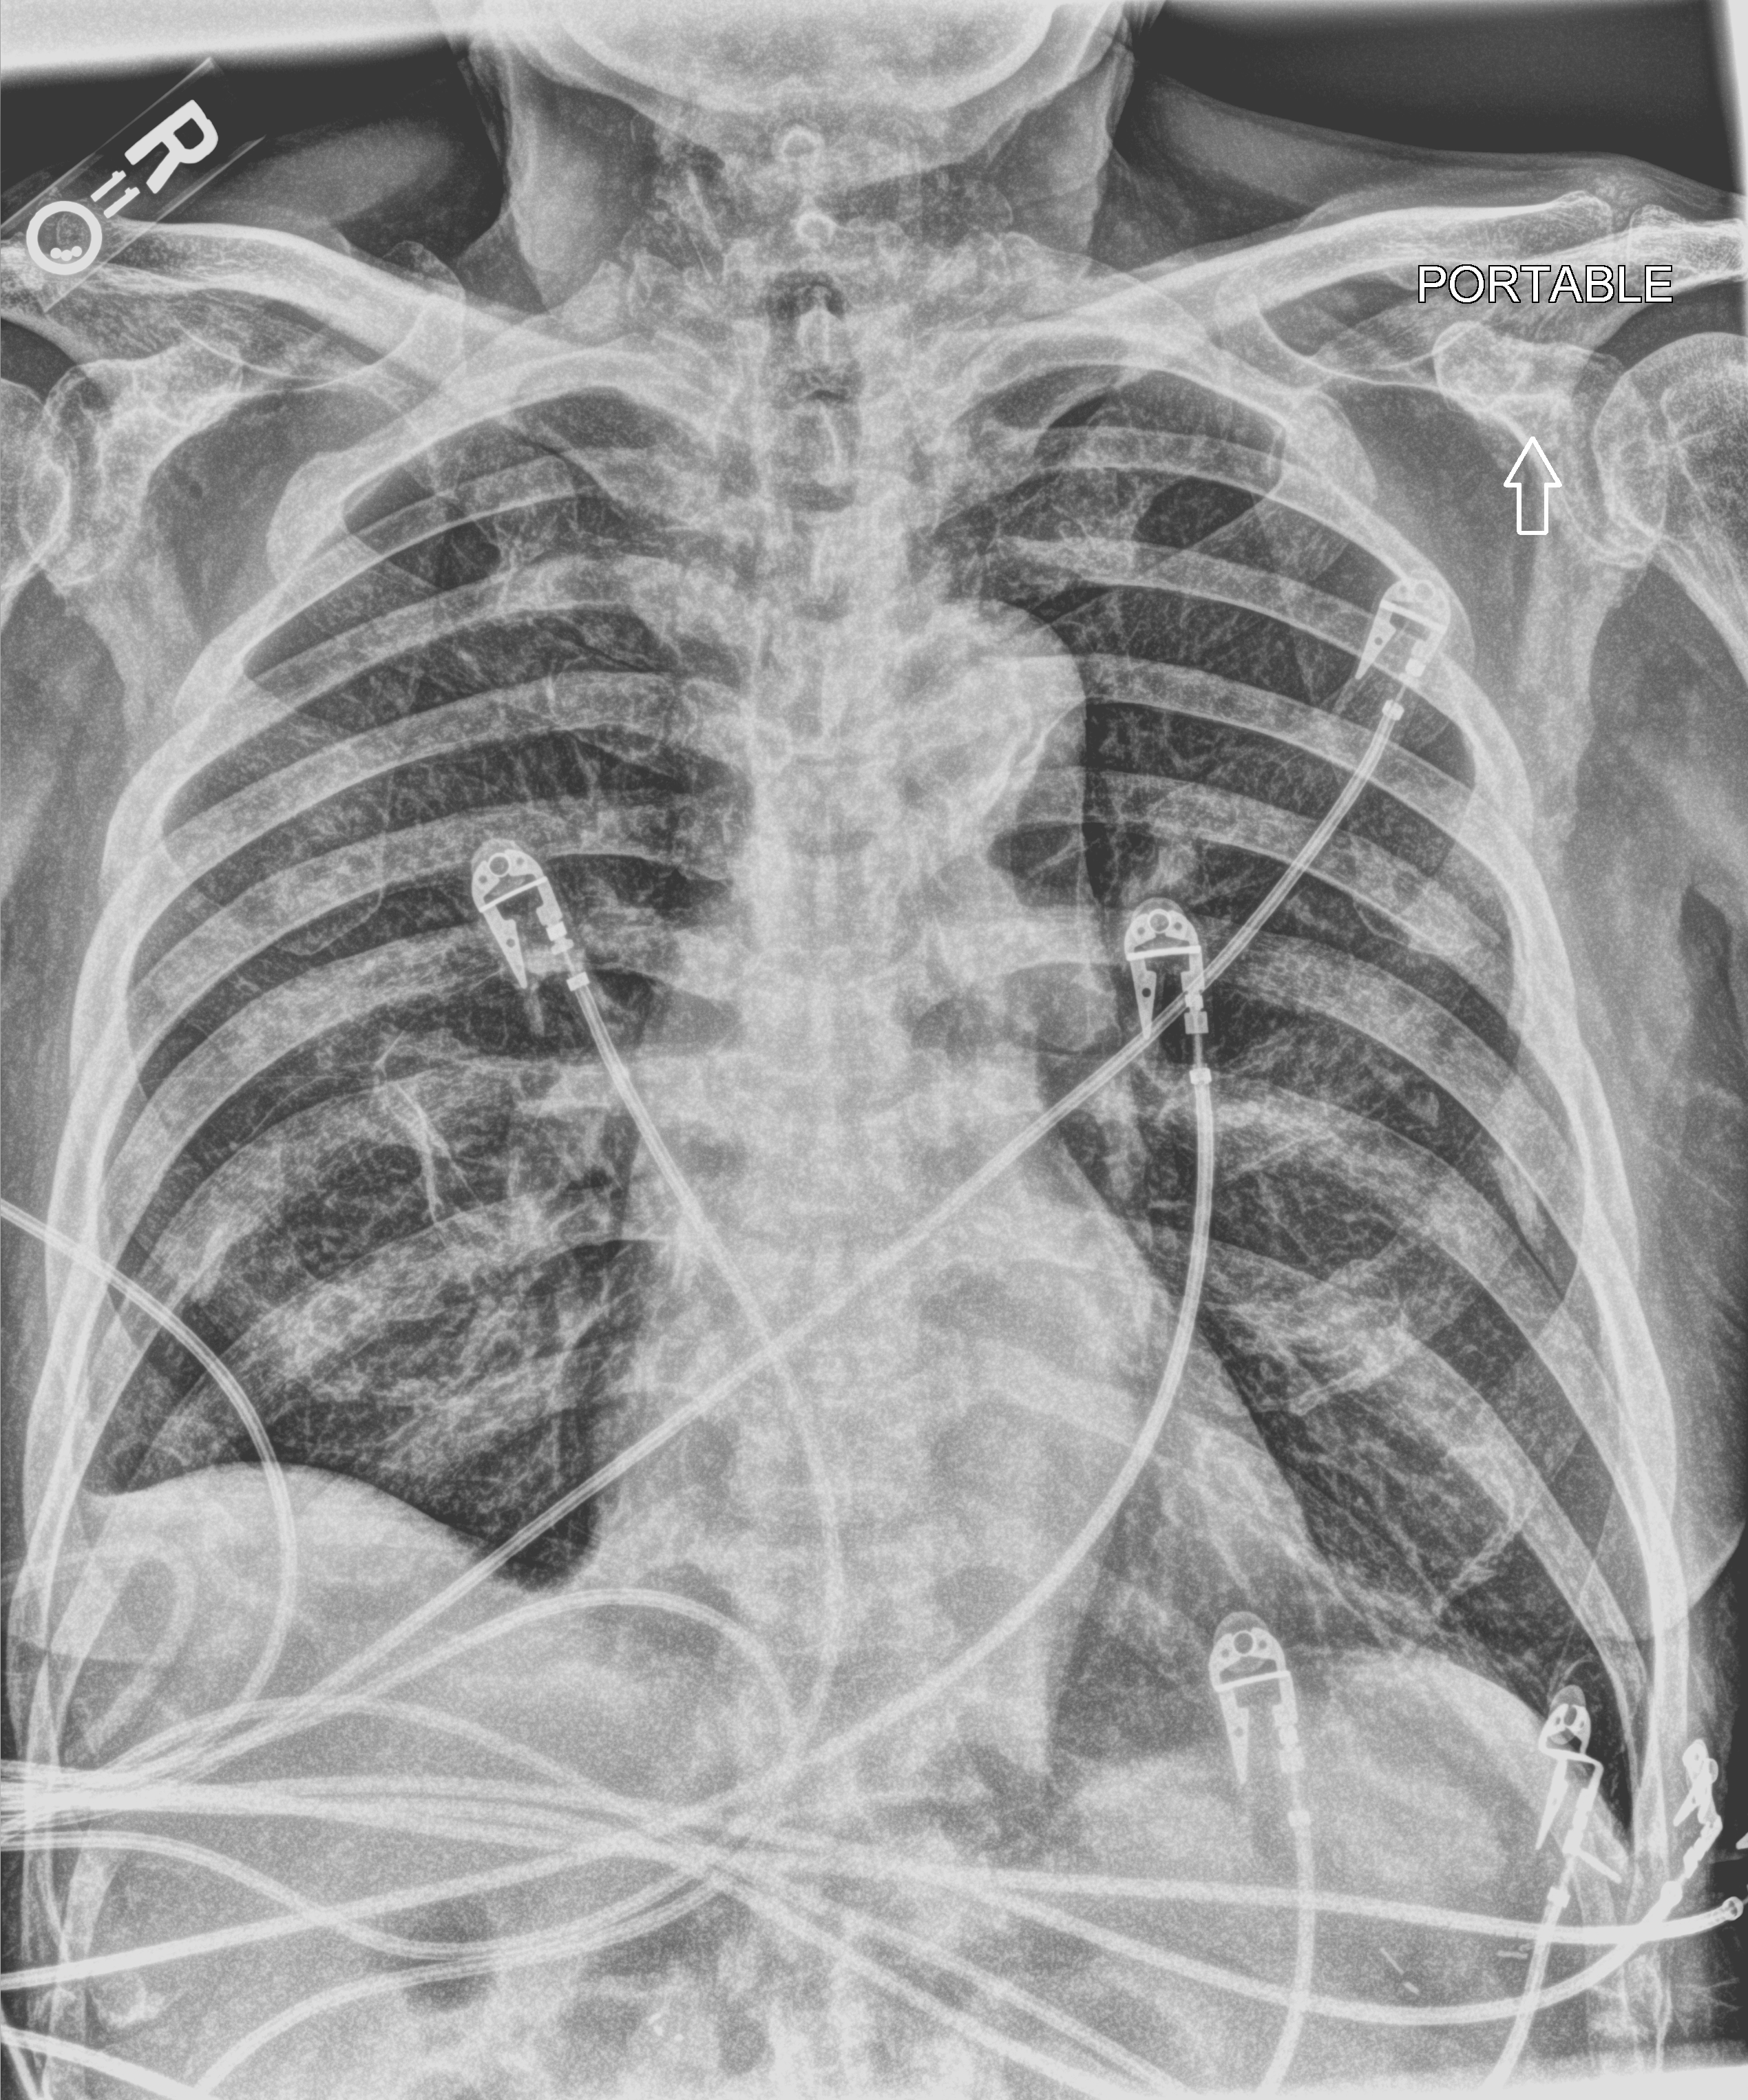
Portable chest radiograph; anteroposterior (AP) projection. Male patient hospitalised with COVID-19, age 75–90 years.
From the hospital-stay record, not from the radiograph (when in the stay this image was taken is not recorded):
- length of hospital stay: 12 days